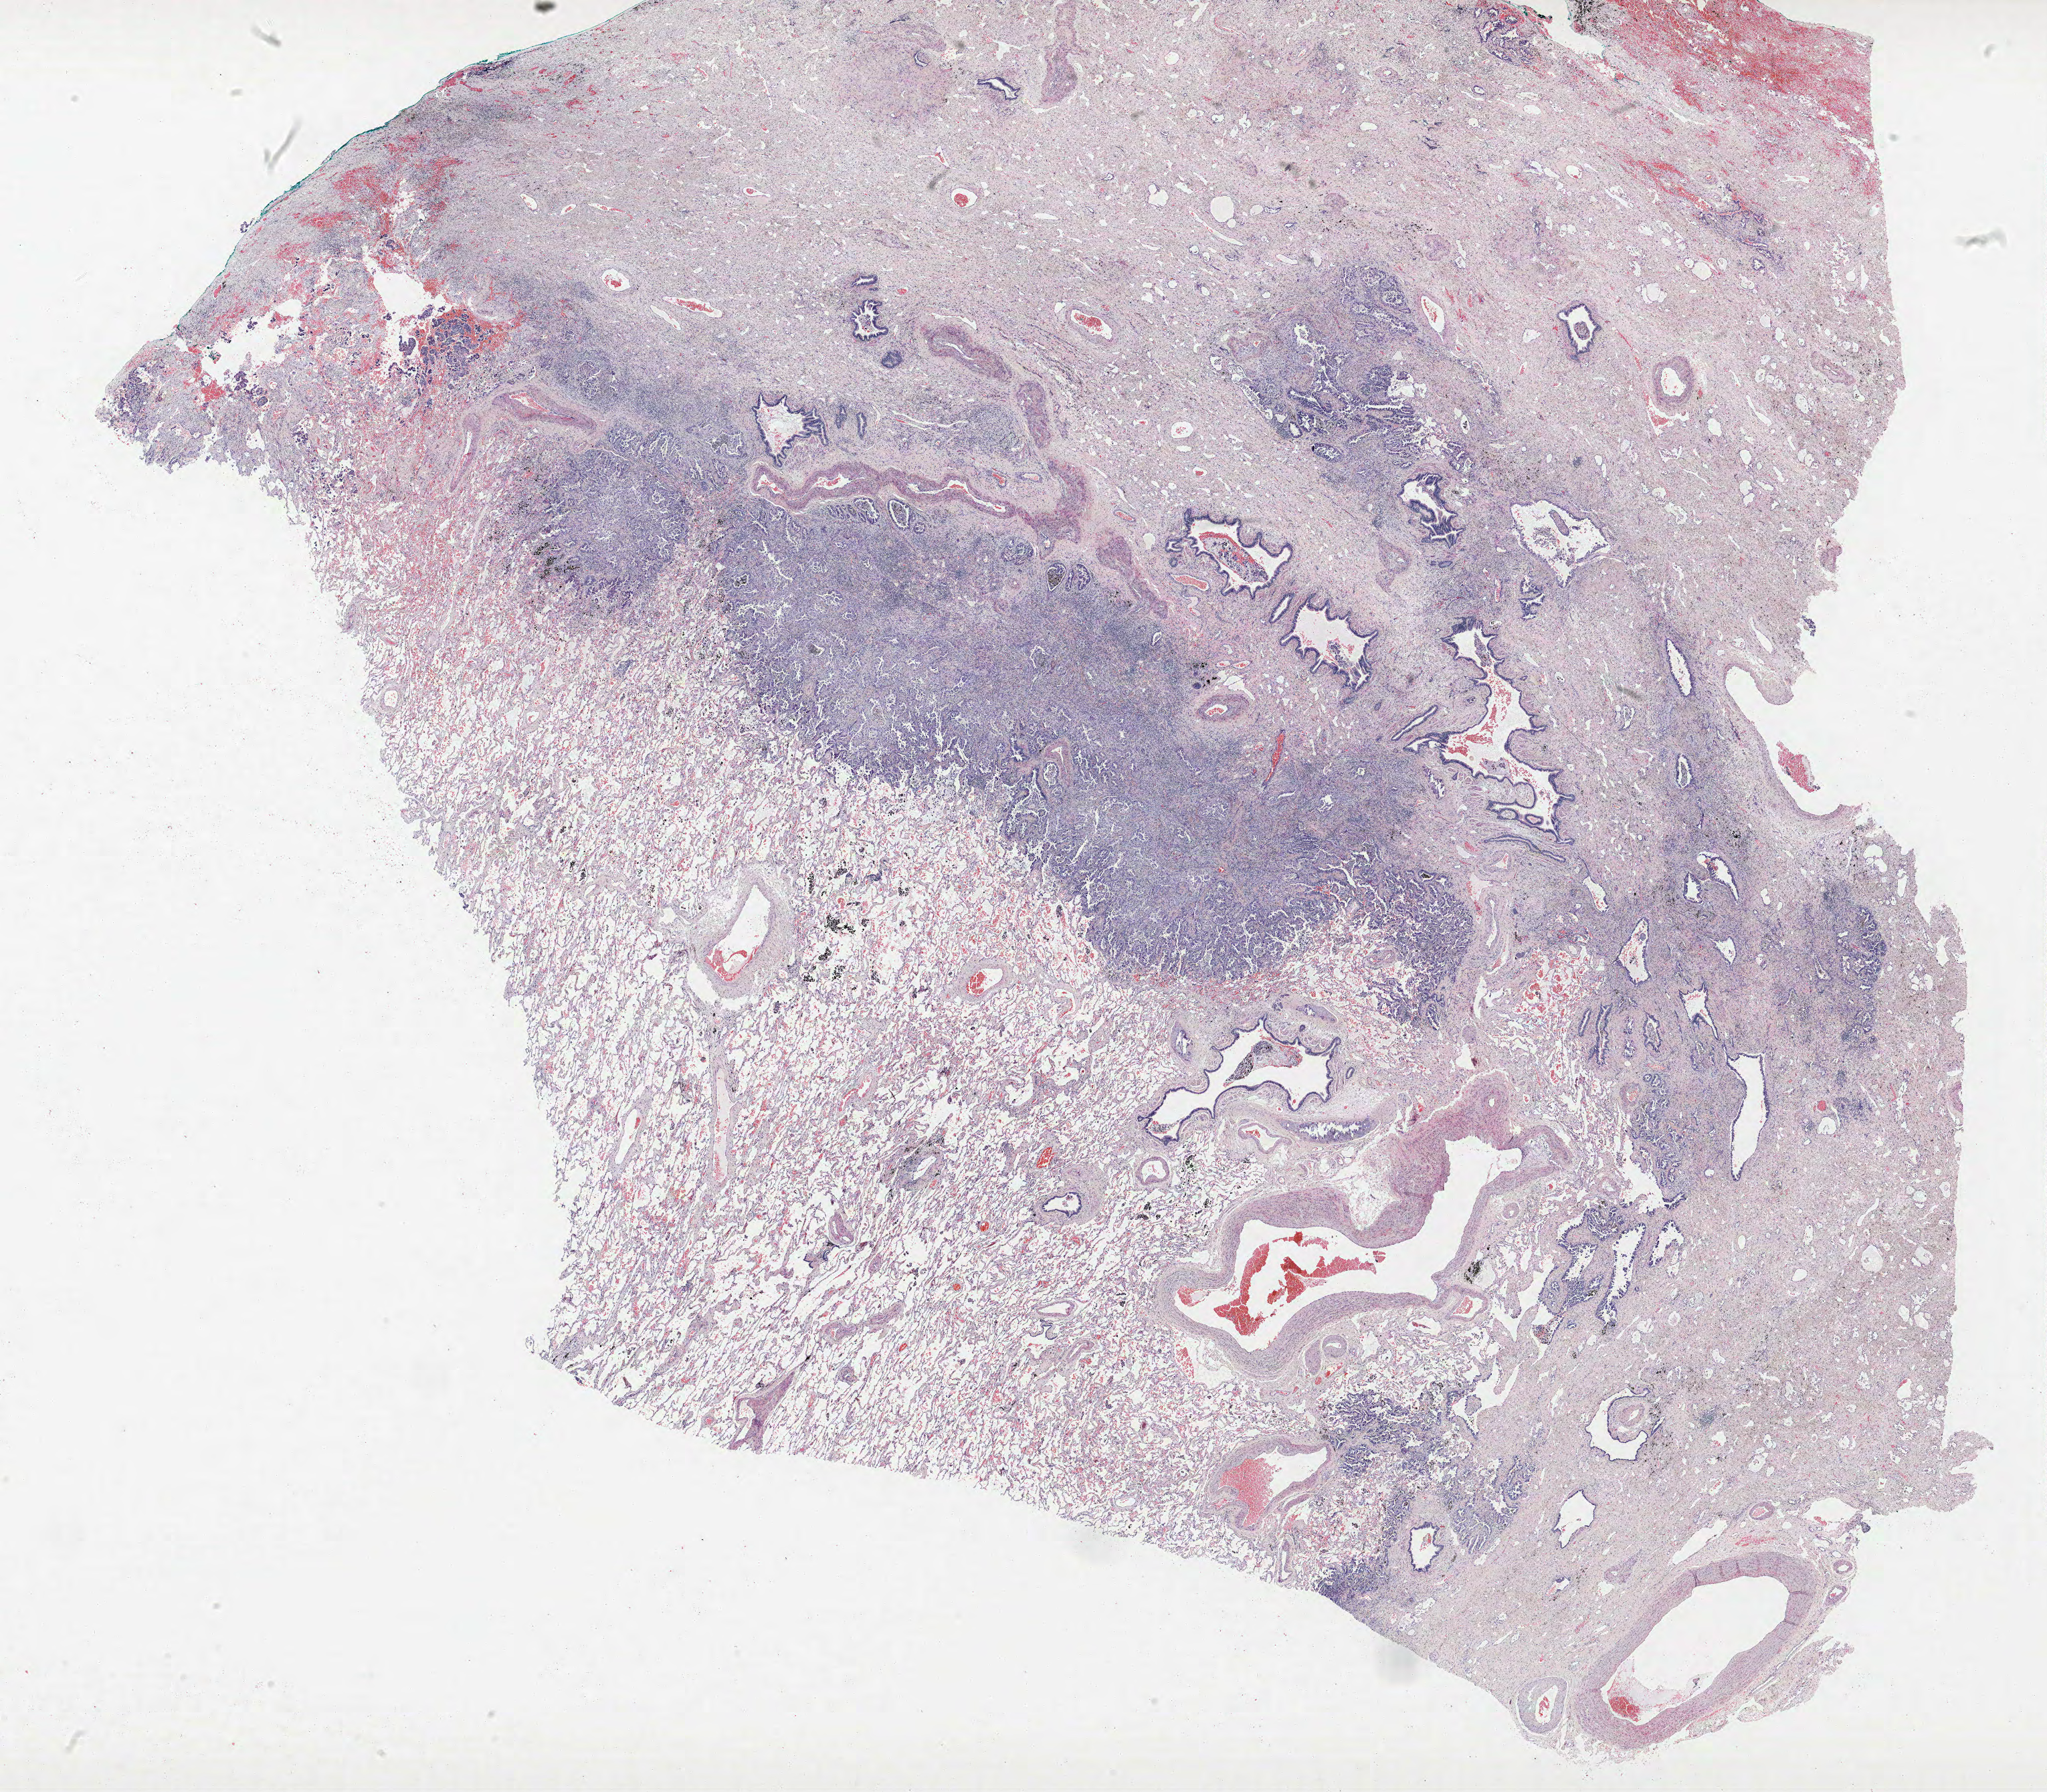
H&E whole-slide image, whole scanned area (about 24.5 x 21.4 mm) shown as a low-resolution overview. FFPE section. Lung. Female, age 68 at enrolment. Grade: poorly differentiated (G3).
- tumour size (pathology): 50 mm
- stage (AJCC 6th edition): IB
- primary tumour location (clinical record): left upper lobe
- participant's lung-cancer diagnosis: Adenocarcinoma, NOS
- ICD-O-3 topography: upper lobe of lung (C34.1)